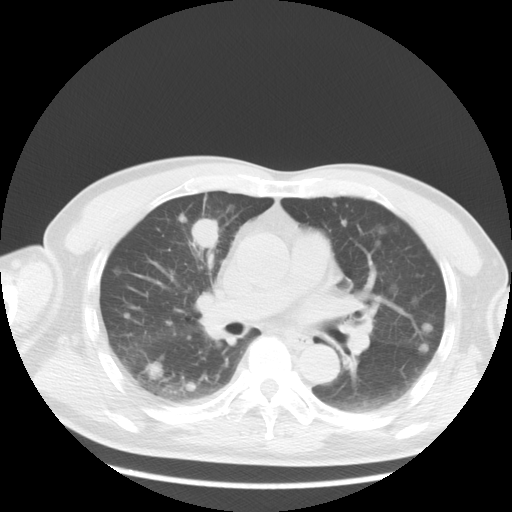
Chest CT, one axial slice. Position 12 of 35 along the scan axis. Reconstruction kernel STANDARD. Lung window (W 1500 / L -600 HU). 5 mm slice thickness. 512 × 512 image matrix, field of view 369 × 369 mm. Patient: male, 57 years. Case-level facts recorded for this patient, not image findings: clinical TNM (as recorded): T2 N3 M1a.
Outlined on this slice (rectangle marked by the reading radiologist):
- lung tumour (recorded histology: adenocarcinoma): box from (x=191, y=216) to (x=217, y=251) px